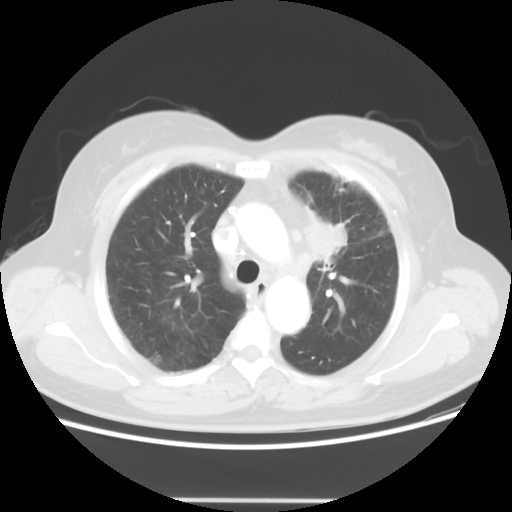
Chest CT, one axial slice. Slice 39 of 52 in the series (ordered by position). 120 kVp. Lung window (W 1500 / L -600 HU). 5 mm slice thickness. 512 × 512 image matrix, field of view 382 × 382 mm. Female patient, age 52 years. From the clinical record (not read from this slice): clinical TNM (as recorded): T2 N3 M0.
Annotated regions visible in this slice (rectangle marked by the reading radiologist):
- lung tumour (recorded histology: adenocarcinoma): bounding box (x1, y1, x2, y2) in pixels: (296, 199, 353, 269)